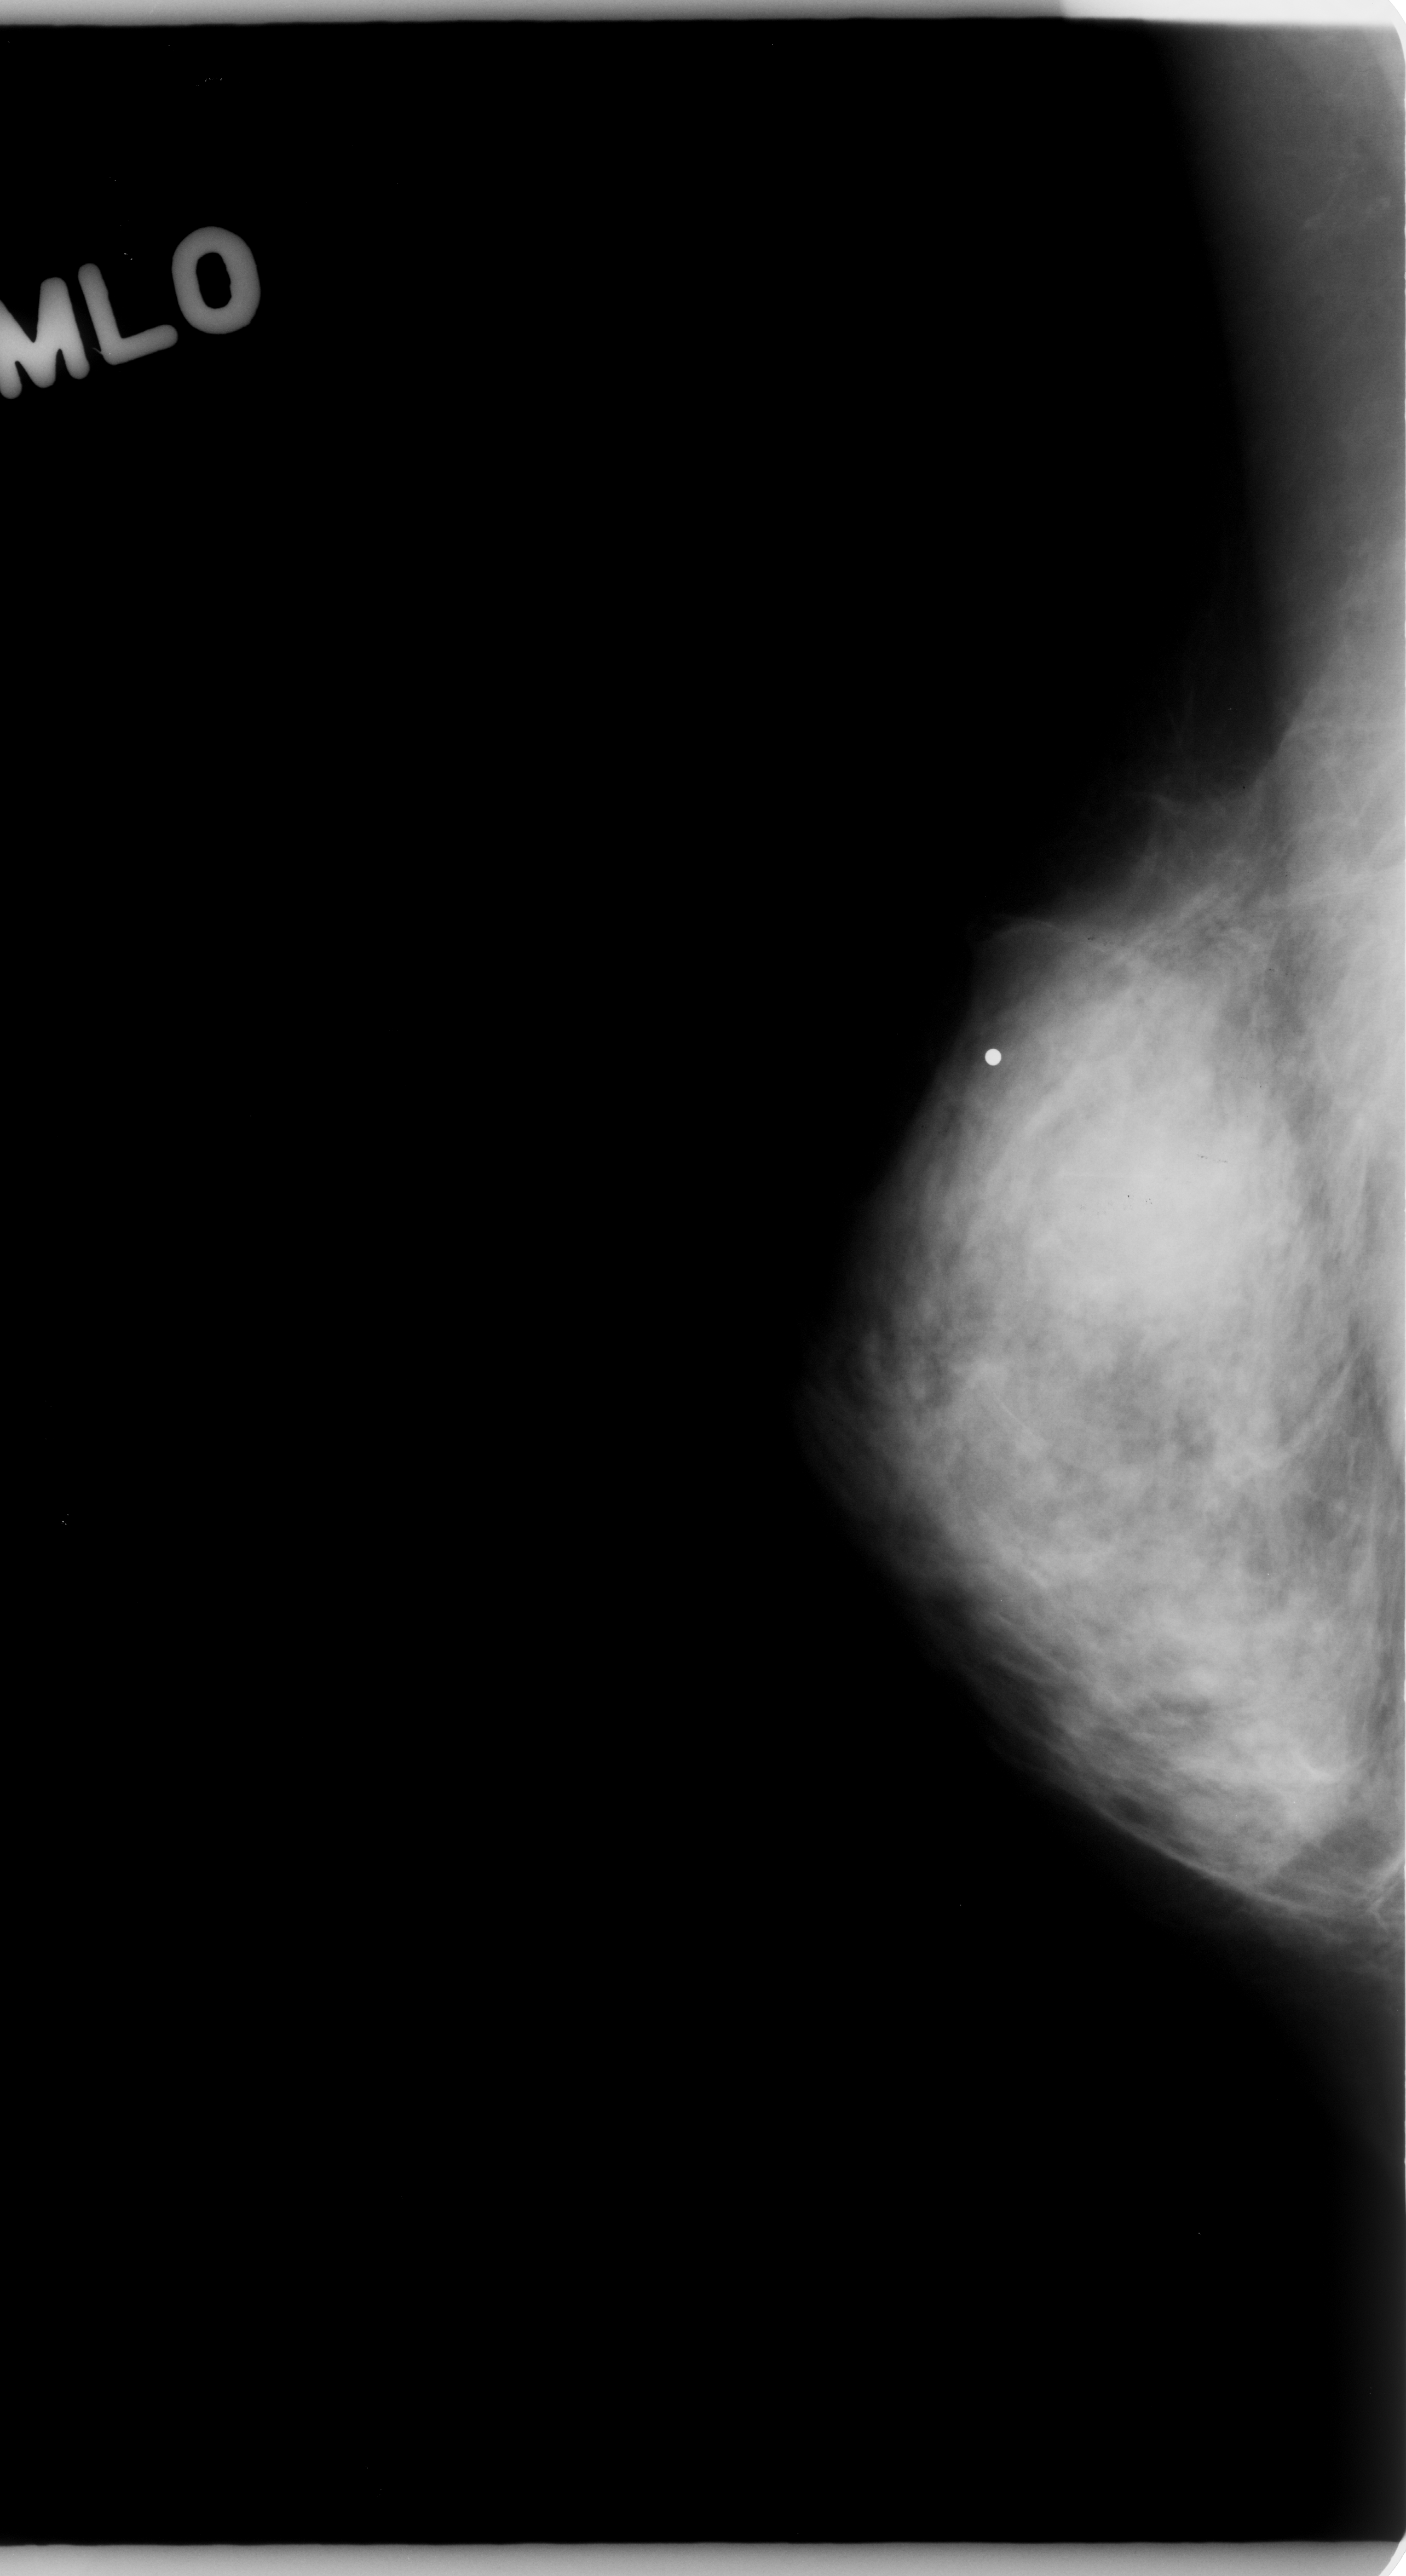
Scanned film-screen mammogram; right breast; mediolateral oblique (MLO) view.
- Radiologist-marked abnormalities on this image: mass, shape round, margins ill defined; BI-RADS assessment category 4; subtlety rating 3 on a 1 (subtle) to 5 (obvious) scale; pathology result (as recorded, not read from the image): malignant.